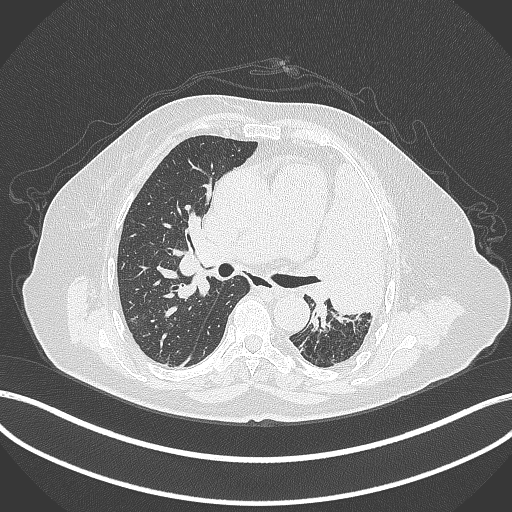
Chest CT, one axial slice. Position 232 of 399 along the scan axis. 120 kVp. Lung window (W 1500 / L -600 HU). 512 × 512 image matrix, field of view 400 × 400 mm. Patient: female, 75 years. Case-level facts recorded for this patient, not image findings: clinical TNM (as recorded): T3 N3 M1.
Structures marked on this image (rectangle marked by the reading radiologist):
- lung tumour (recorded histology: adenocarcinoma): box from (x=314, y=161) to (x=394, y=318) px